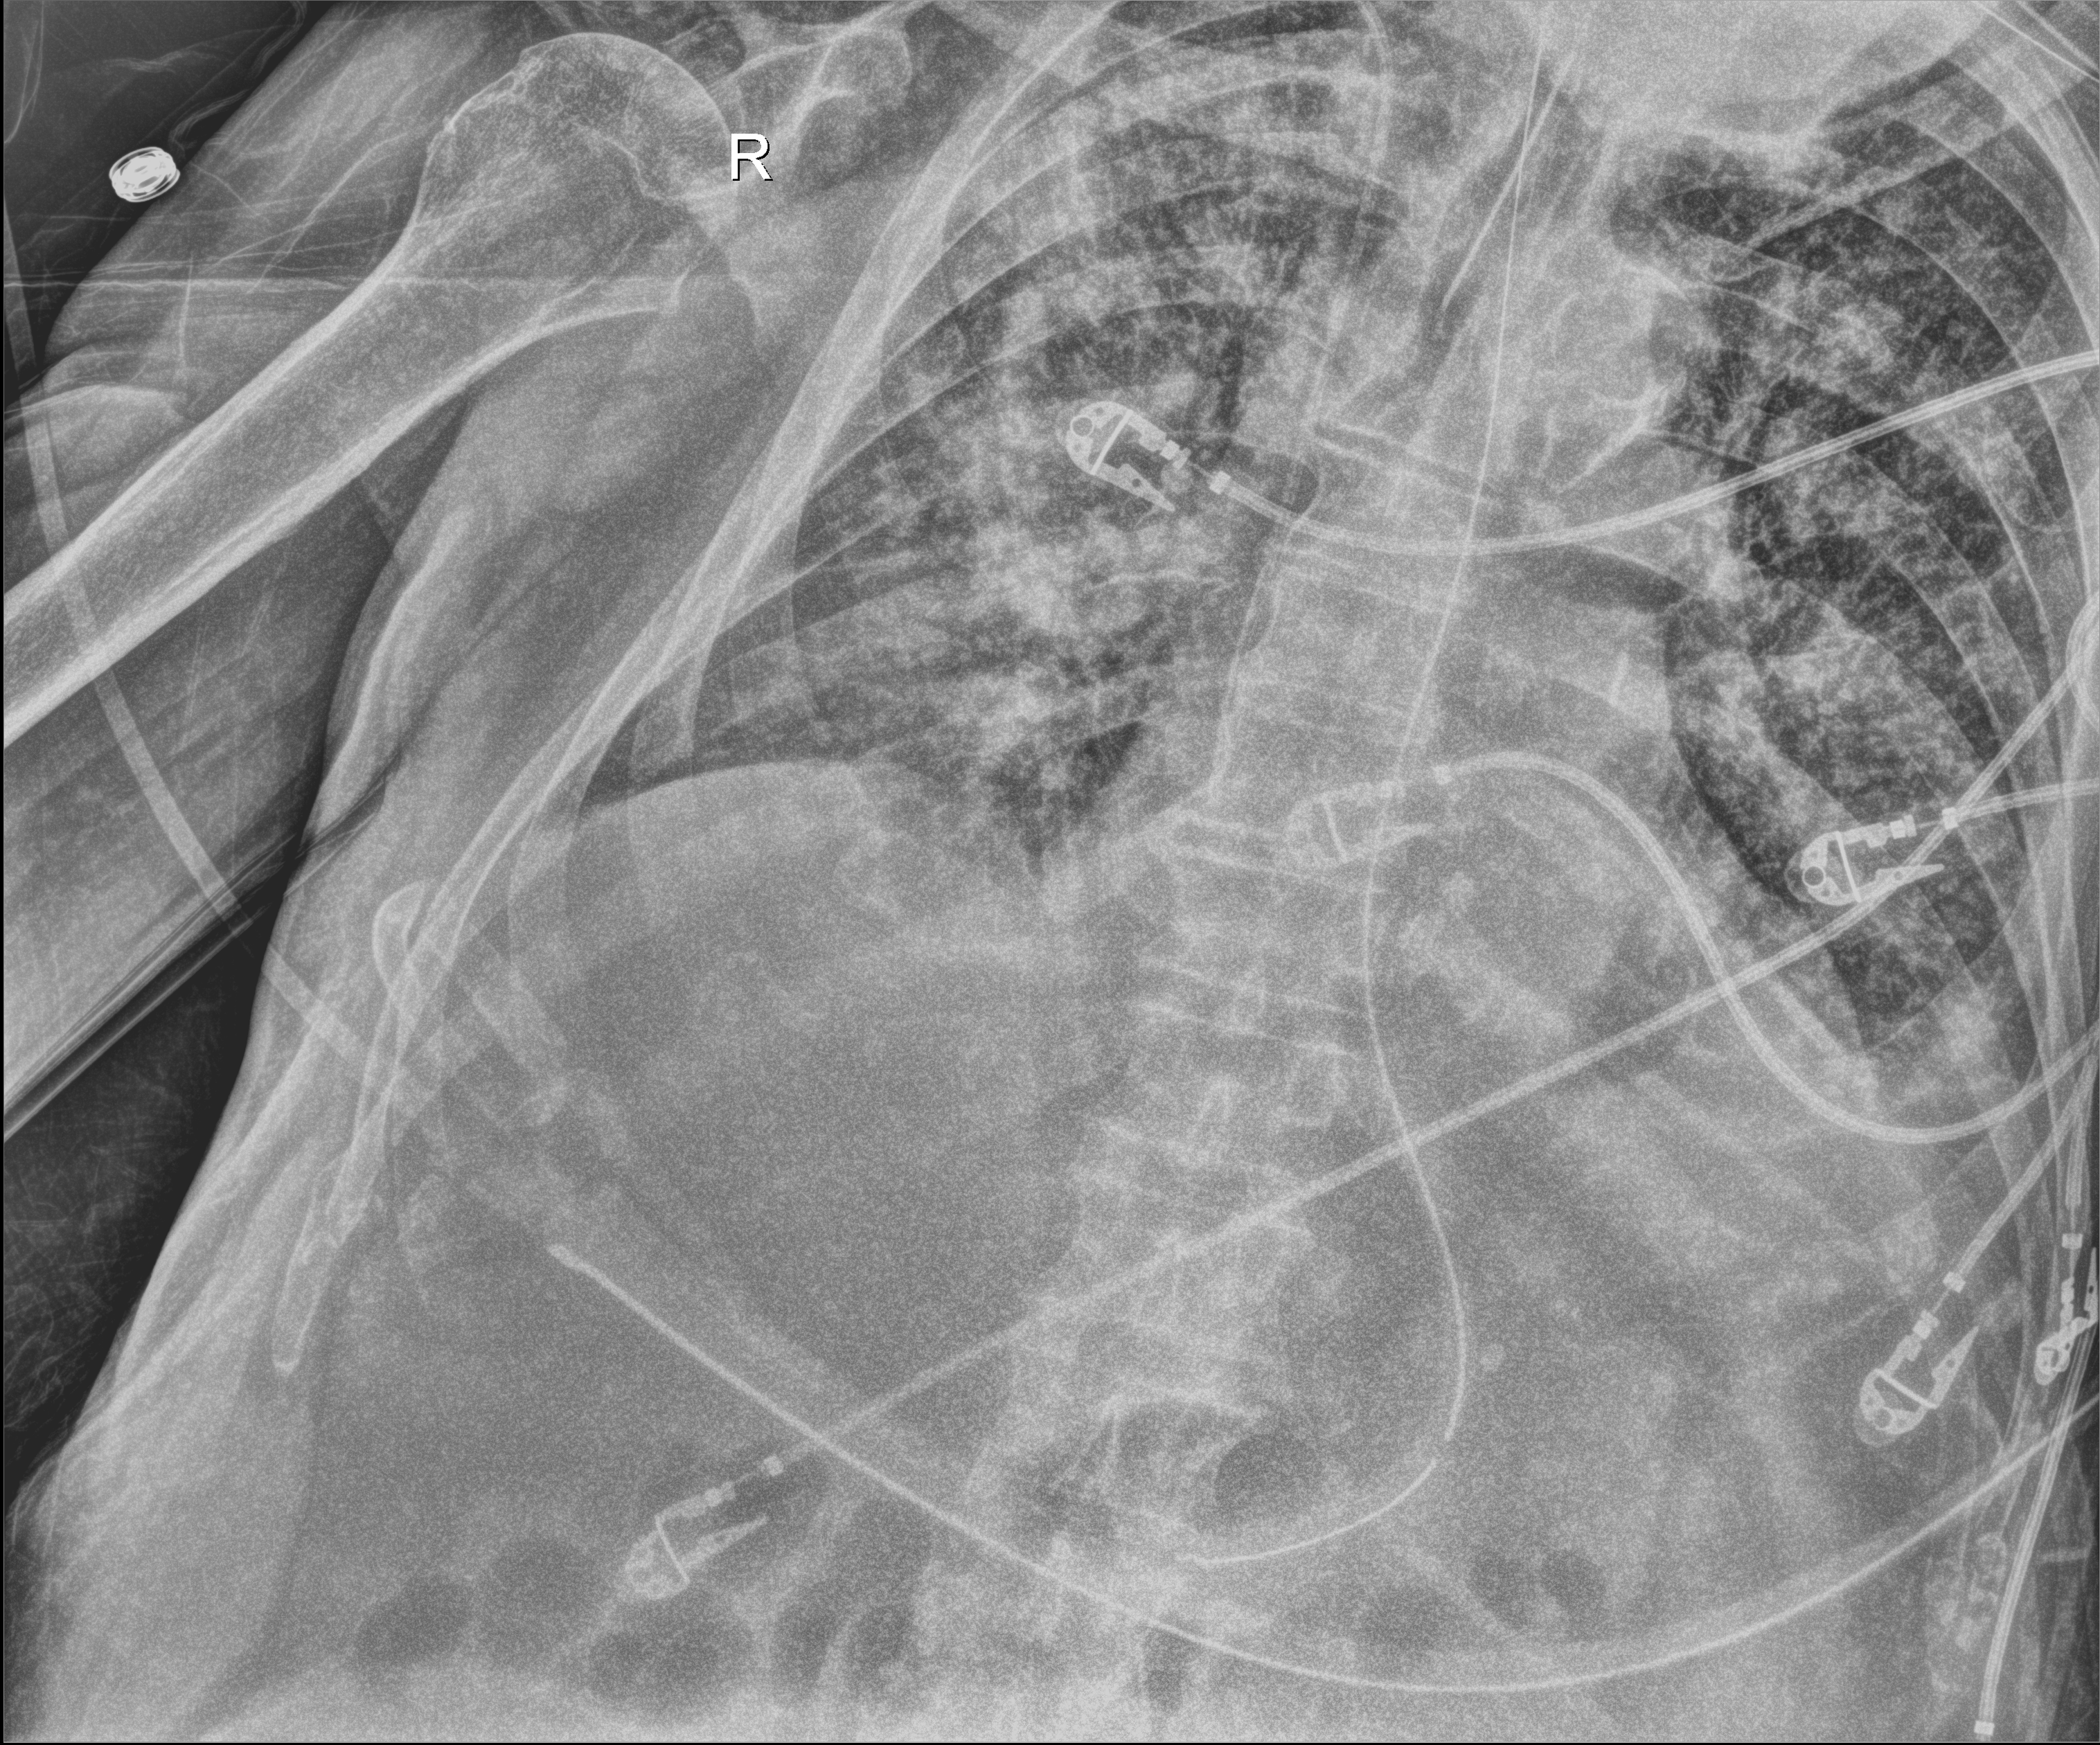
Bedside chest radiograph (digital radiography). Male patient hospitalised with COVID-19, age 75–90 years.
Admission-level facts for this patient (not findings on this image; timing relative to this image not recorded):
- smoking status (admission record): never
- admitted to intensive care during this hospital stay: yes